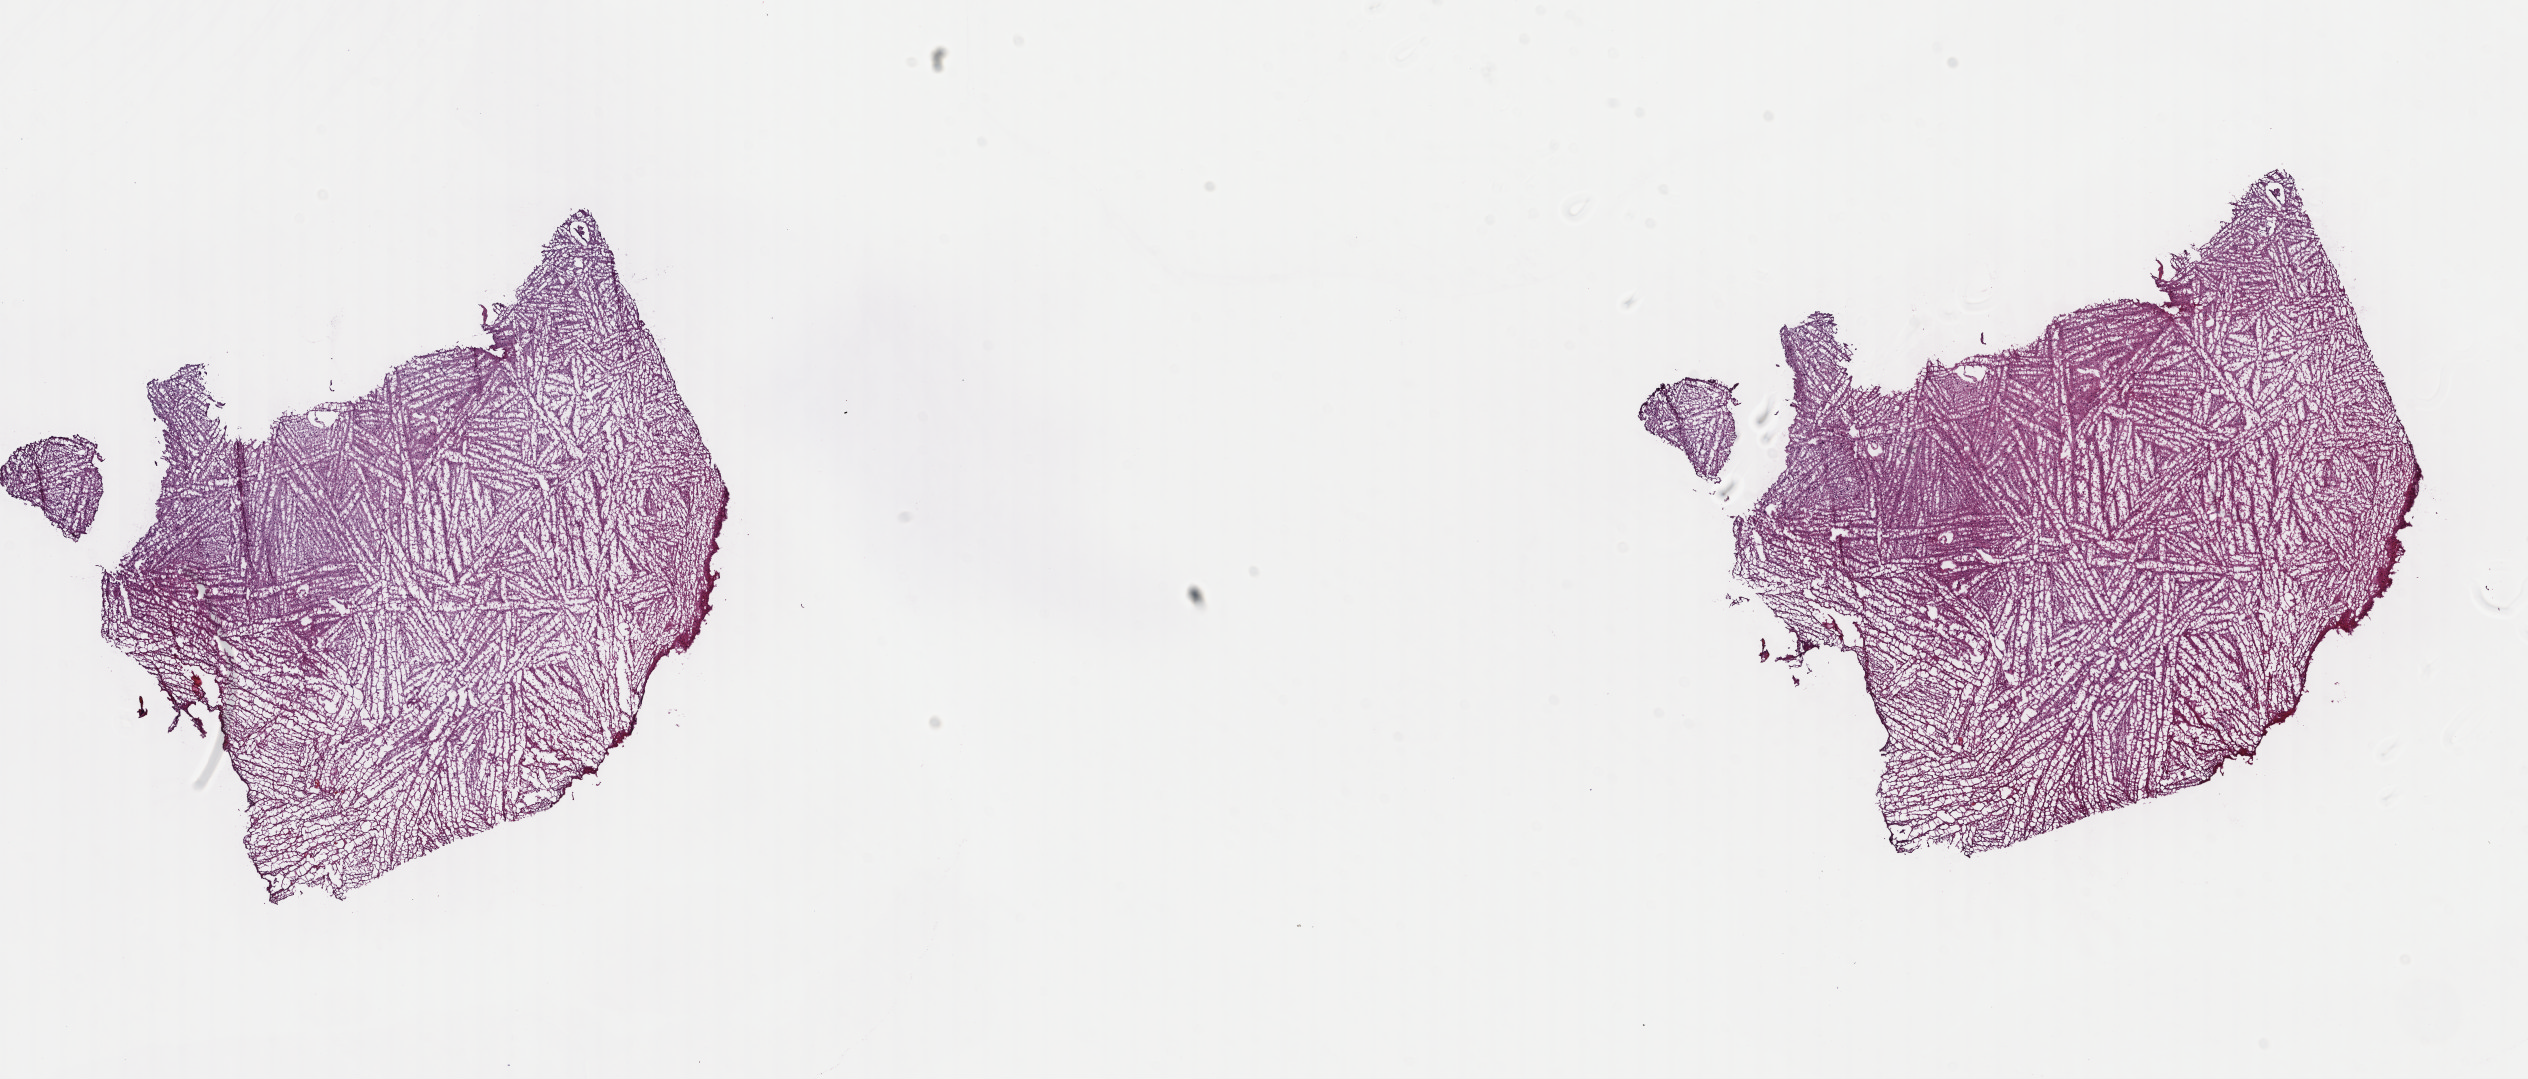
Whole-slide histology image, Hematoxylin and eosin (H&E) stained, a low-resolution overview of the entire scanned area, about 19.9 x 8.5 mm. Frozen section. Primary tumour sample from the brain. Patient: male, age at initial diagnosis 30 years. Histologic grade: G2 (moderately differentiated). Slide review estimates, as recorded: tumour cells 50%, tumour nuclei 80%, normal cells 10%, stromal cells 40%, necrosis 0%. Inflammatory infiltration, as recorded: lymphocyte infiltration 0%, monocyte infiltration 0%, neutrophil infiltration 0%.
Laterality: left. Diagnosis: Astrocytoma, NOS (cerebrum).